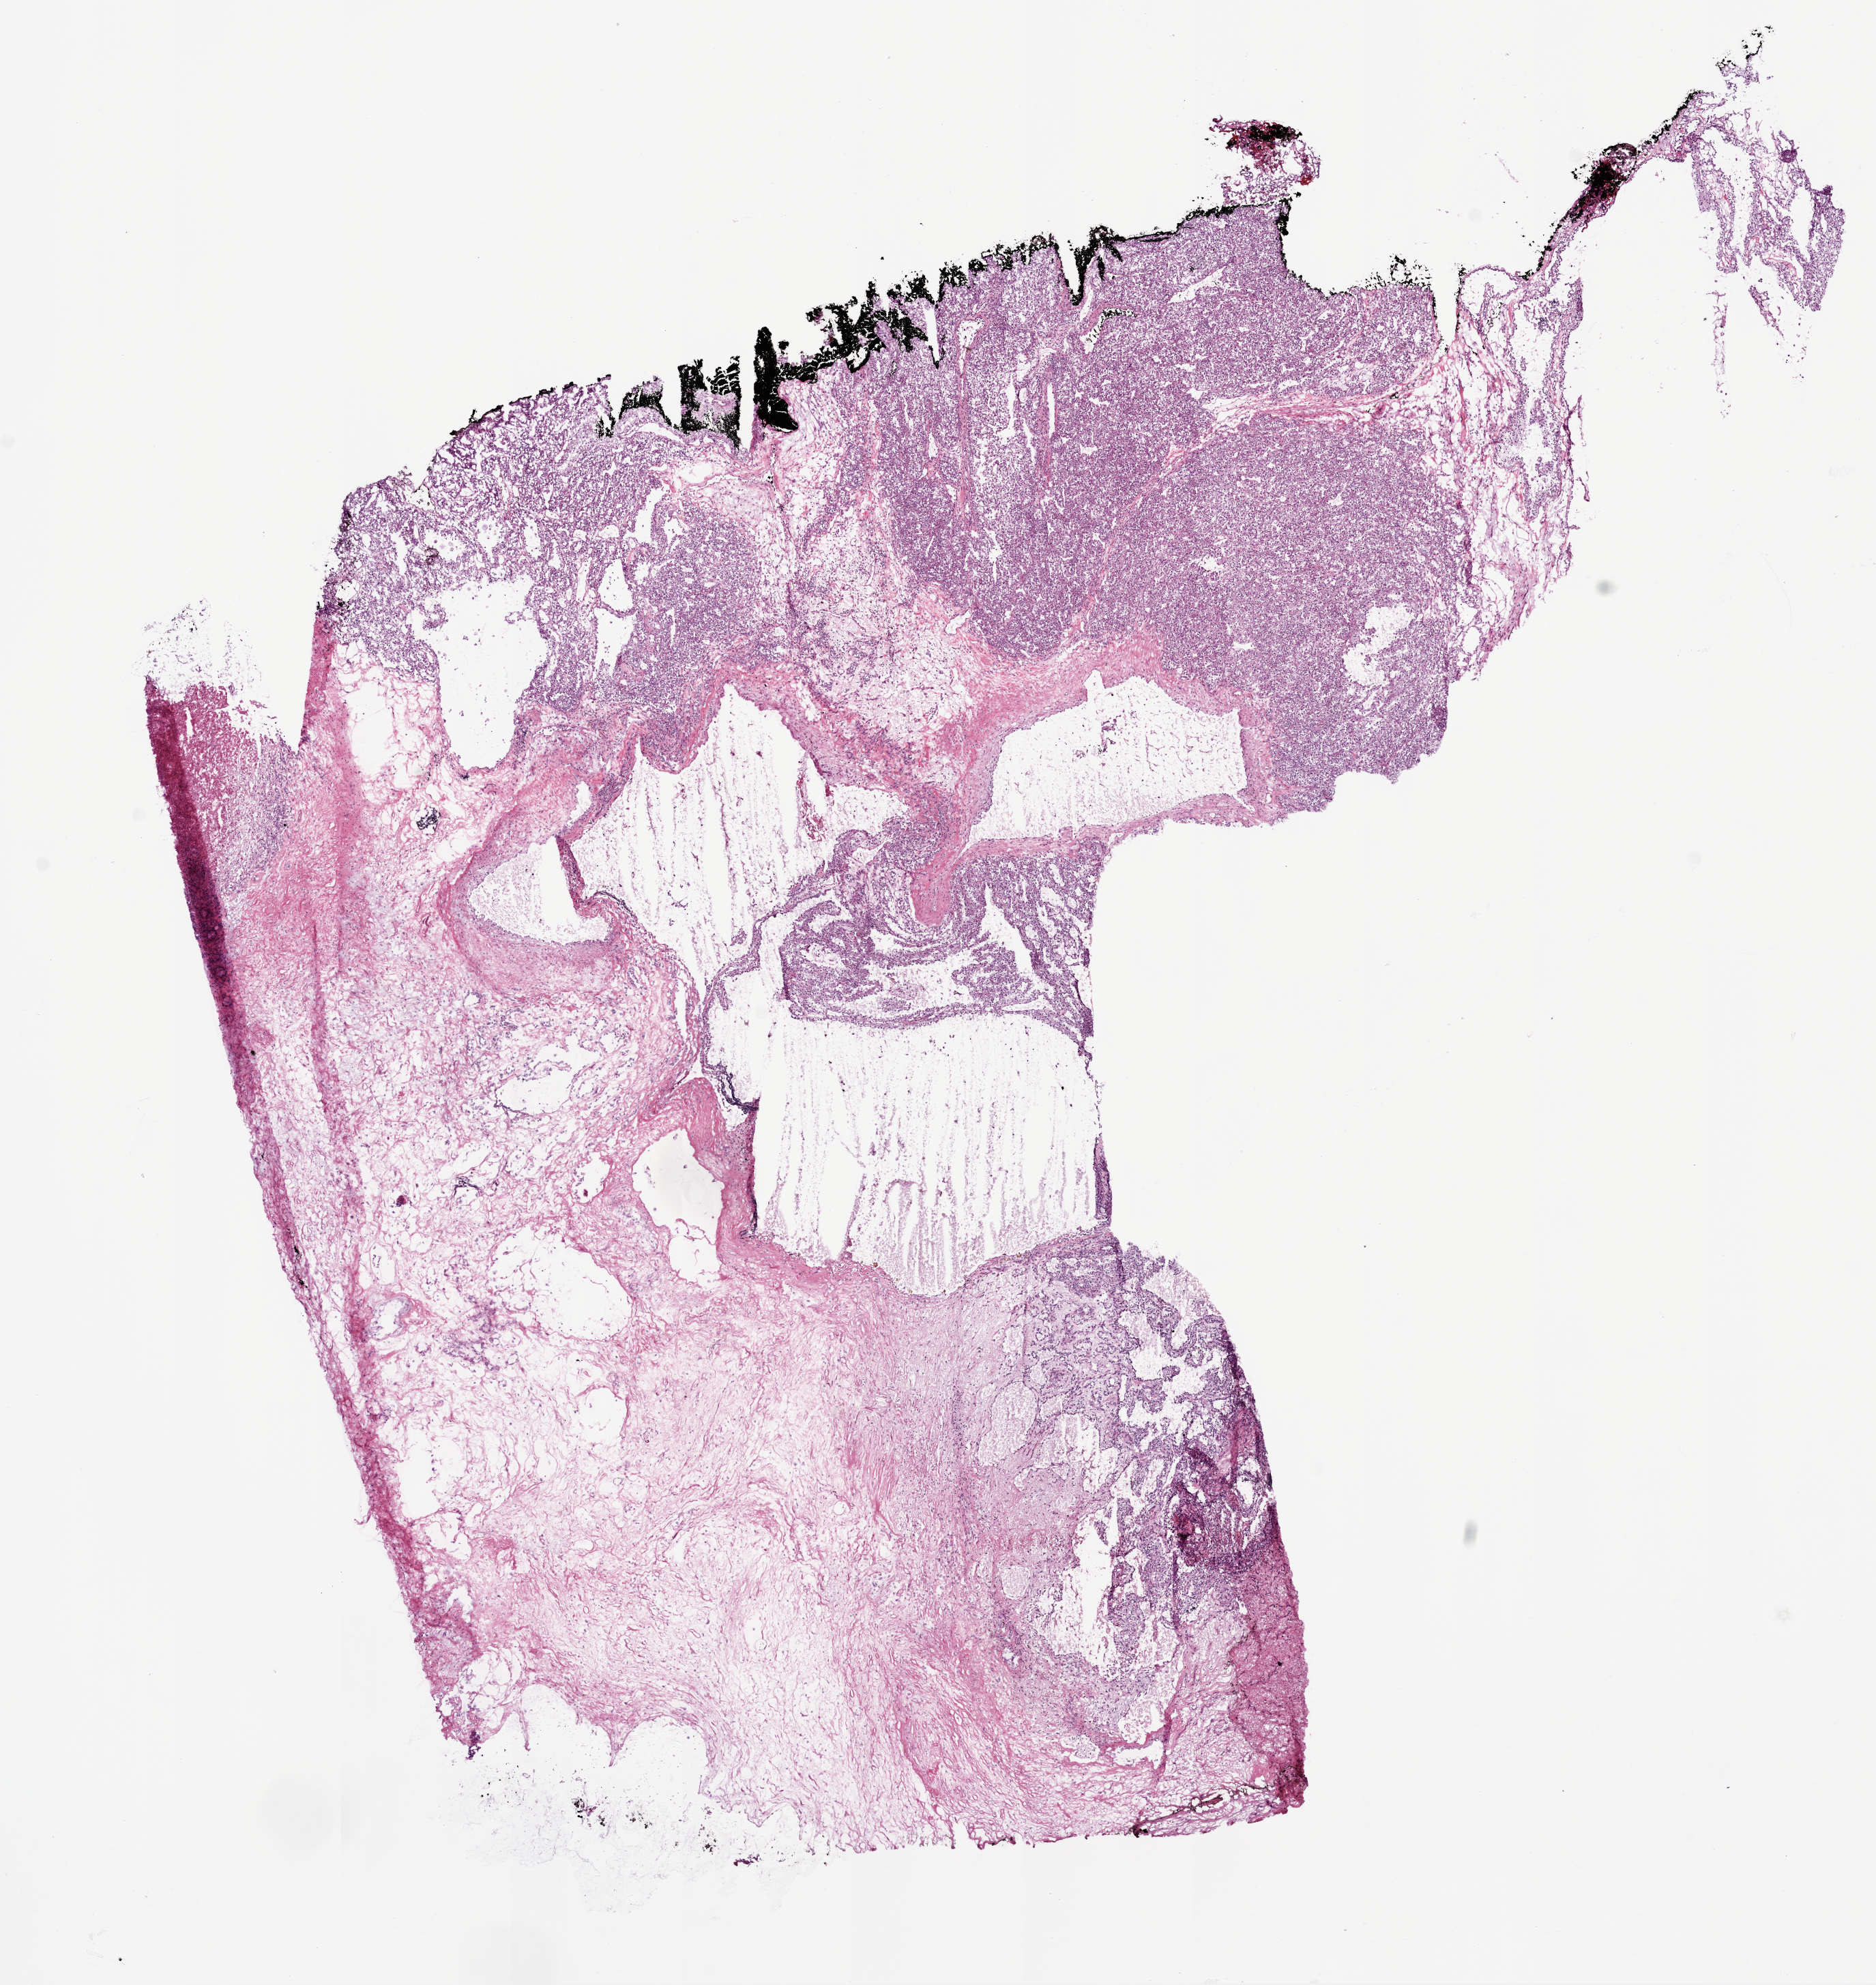
Whole-slide histology image, Hematoxylin and eosin (H&E) stained — low-resolution overview of the scanned area, about 11.0 x 11.7 mm (from a 20x scan); frozen section from the bottom of the tissue portion; sample: primary tumour, kidney. Male, age 51 years at initial diagnosis. Histologic grade: G3 (poorly differentiated). Slide review estimates, as recorded: tumour cells 45%, tumour nuclei 80%, normal cells 0%, stromal cells 55%, necrosis 0%.
• diagnosis: Clear cell adenocarcinoma, NOS
• laterality: right
• AJCC pathologic stage: I